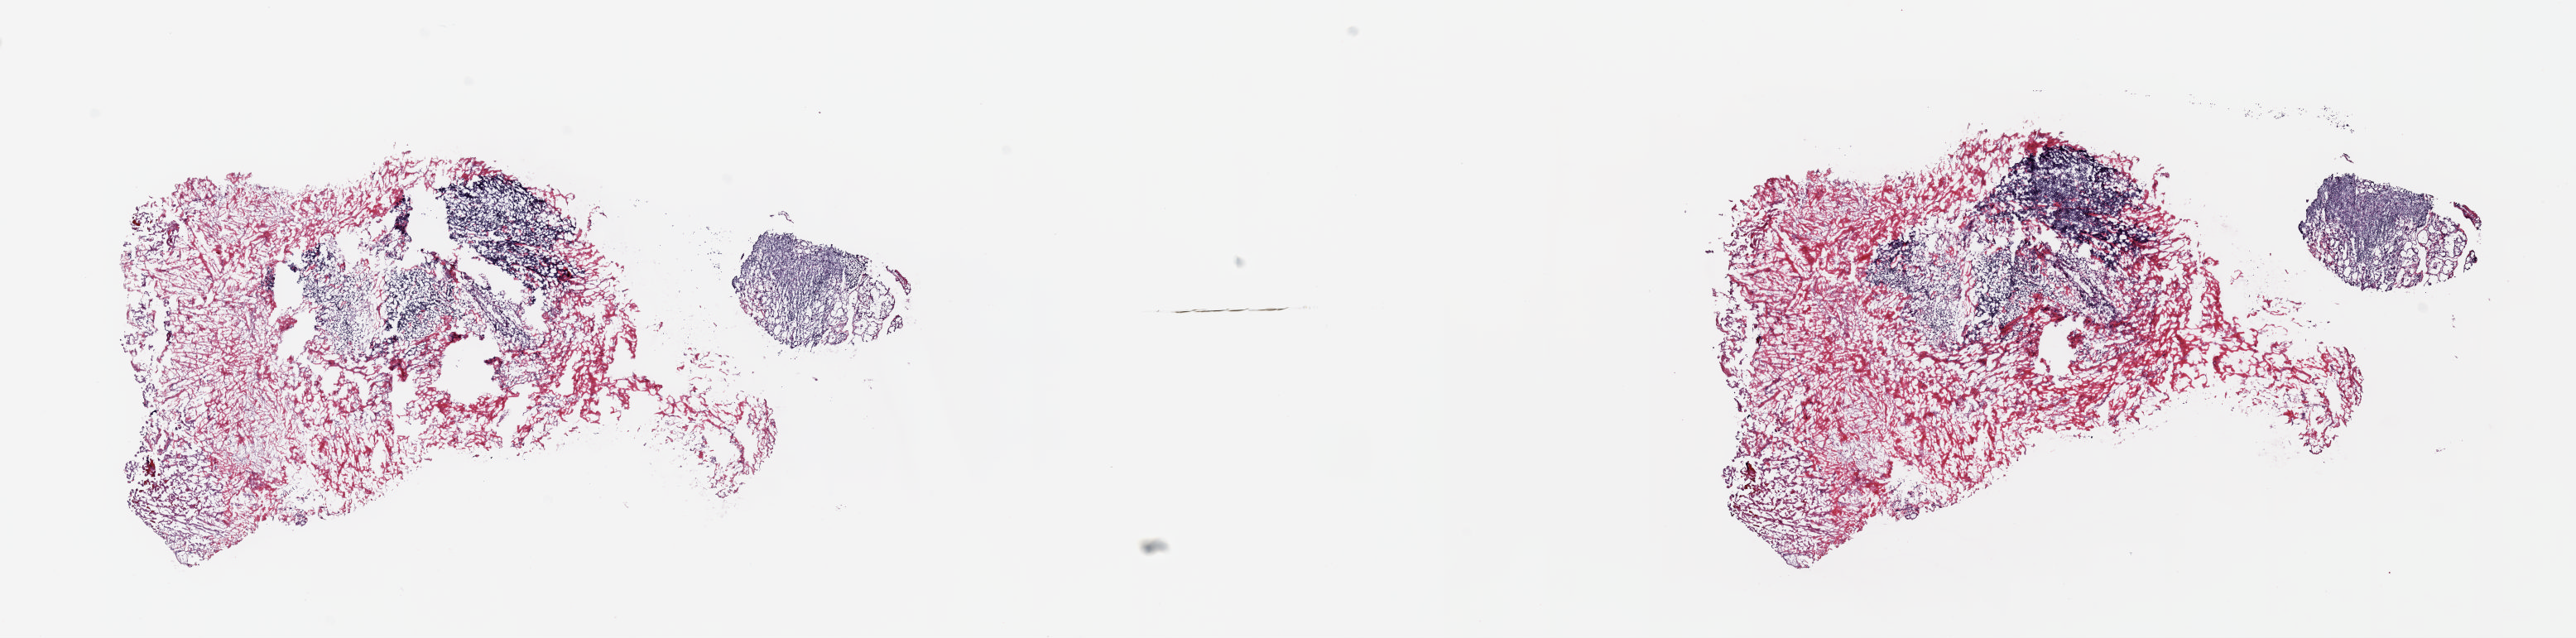
Whole-slide histology image, H&E-stained, a low-resolution overview of the entire scanned area, about 24.5 x 6.1 mm, frozen section from the top of the tissue portion, thyroid, solid tissue normal (non-tumour tissue) sample. Patient: female, age at initial diagnosis 22 years. Slide review estimates, as recorded: tumour cells 0%, tumour nuclei 0%, normal cells 0%, stromal cells 100%, necrosis 0%. Infiltration values recorded for this section: lymphocyte infiltration 50%, monocyte infiltration 0%, neutrophil infiltration 0%.
* this section: solid tissue normal sample (biorepository sample class)
* patient diagnosis: Papillary adenocarcinoma, NOS (thyroid gland)